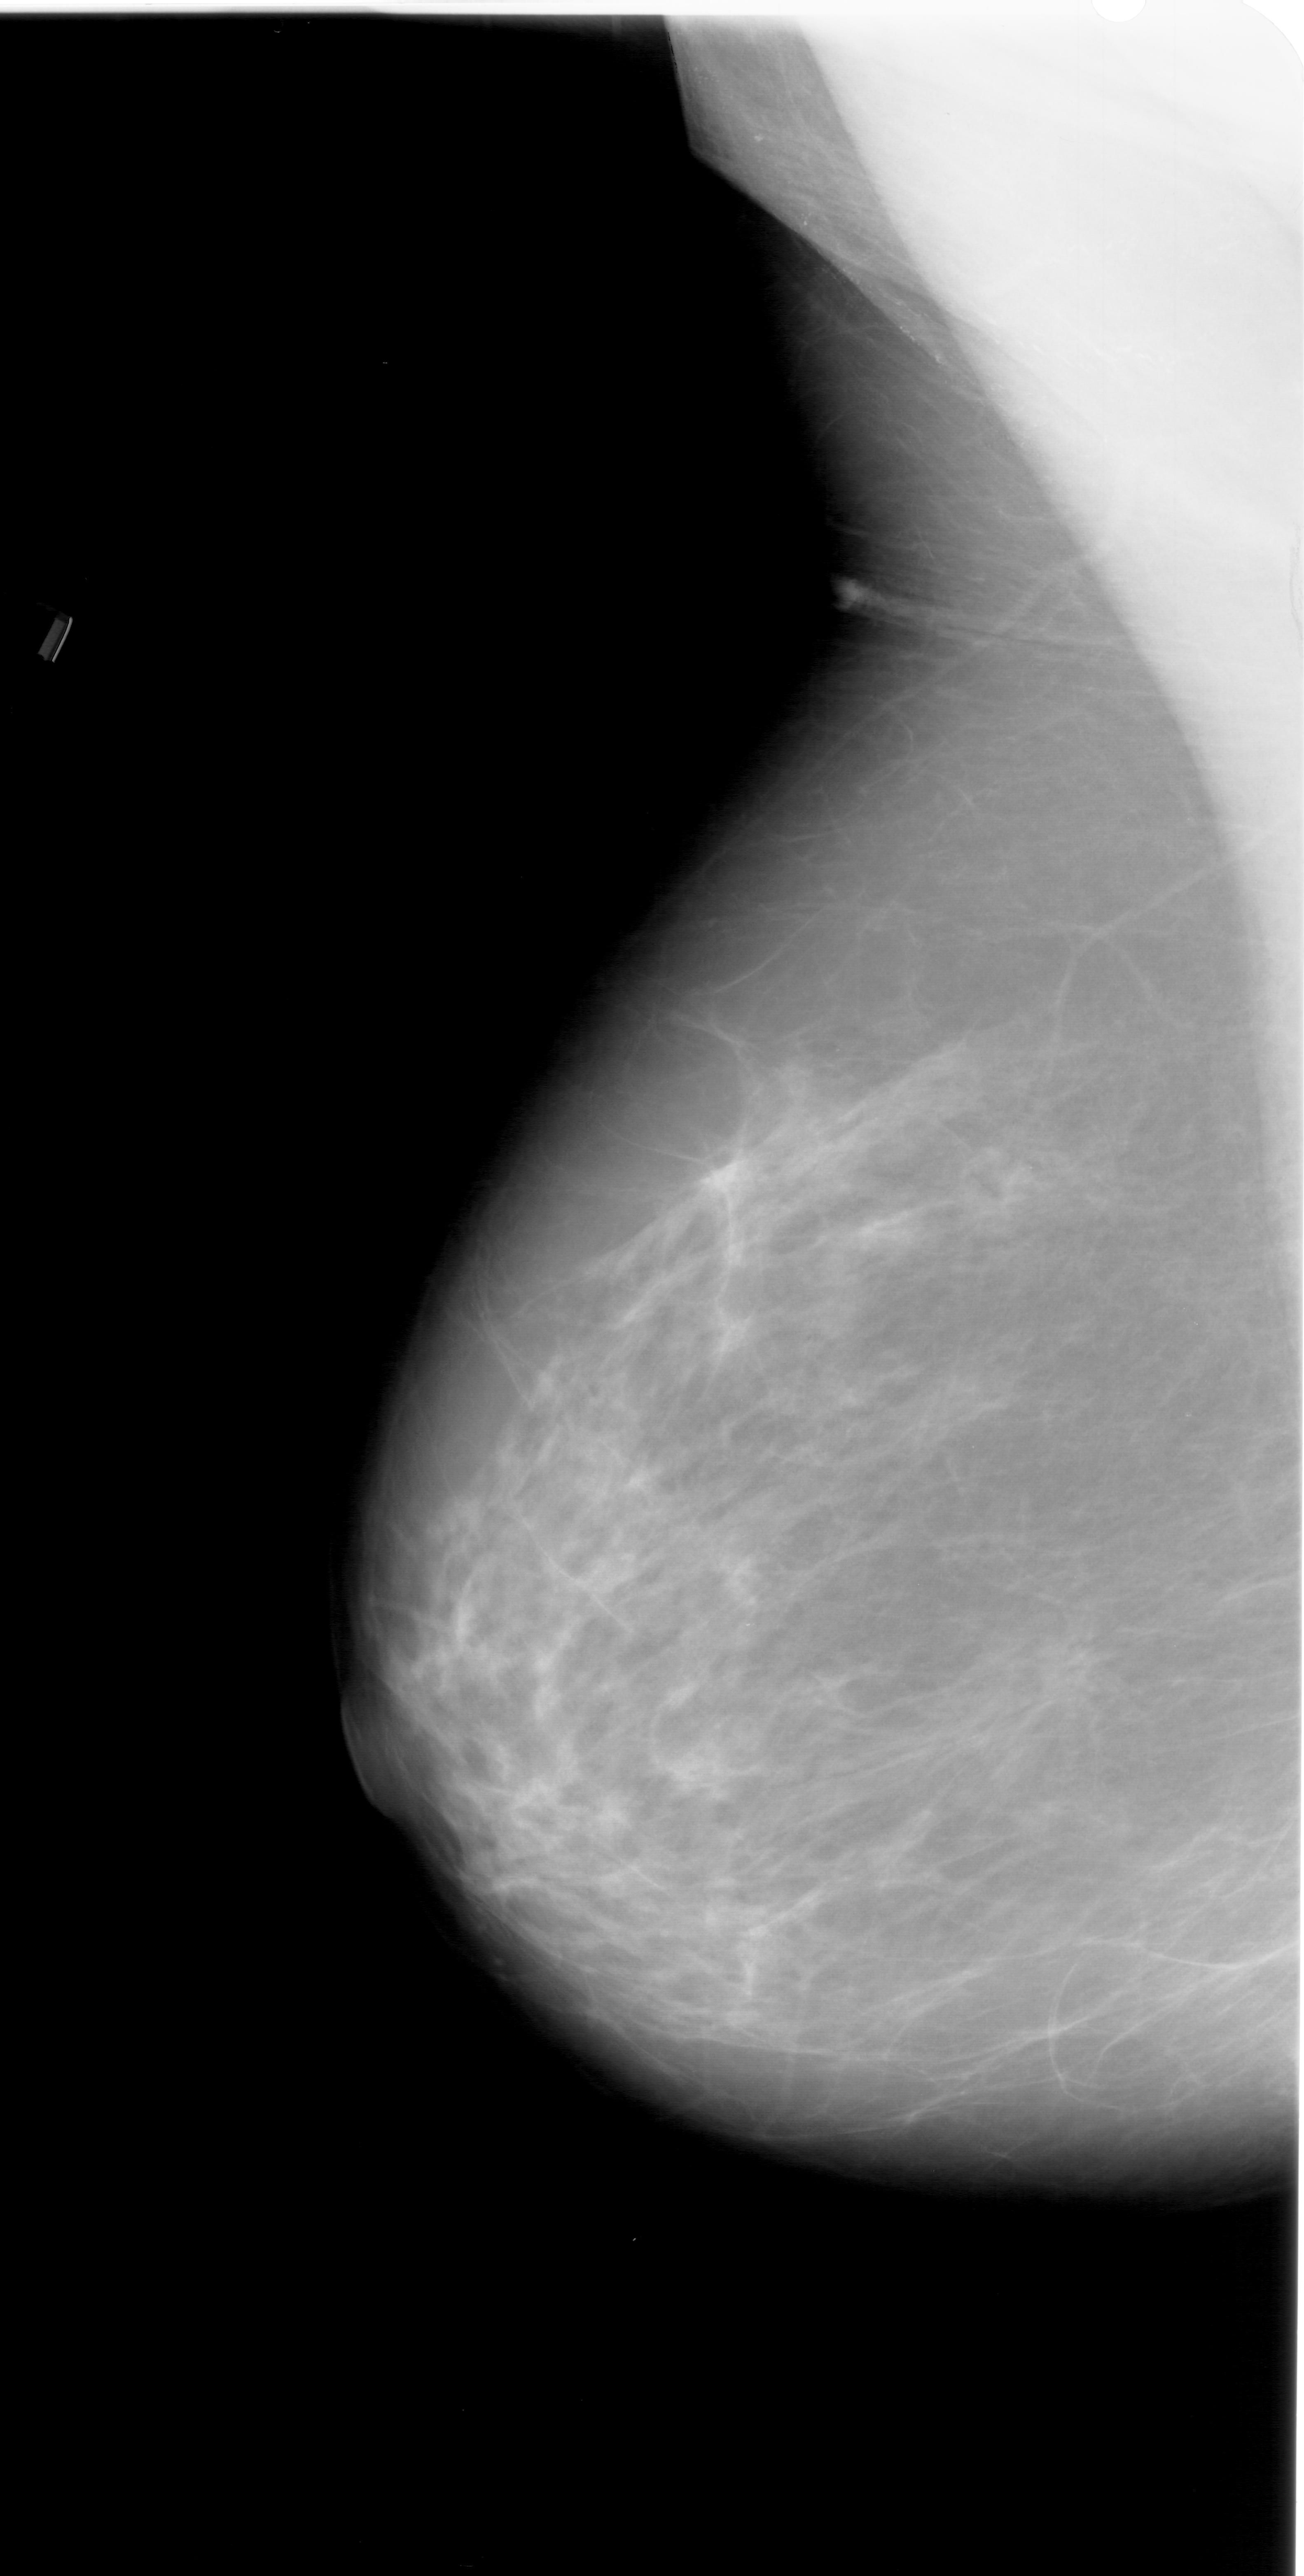
Digitized screen-film mammogram. Left breast. Mediolateral oblique (MLO) view. 1304 × 2576 image matrix.
Expert-marked regions of interest on this film, with their recorded descriptors:
- mass, shape architectural distortion, margins ill defined; BI-RADS assessment category 4; subtlety rating 2 on a 1 (subtle) to 5 (obvious) scale; pathology (as recorded): benign: box from (x=969, y=1611) to (x=1127, y=1748) px